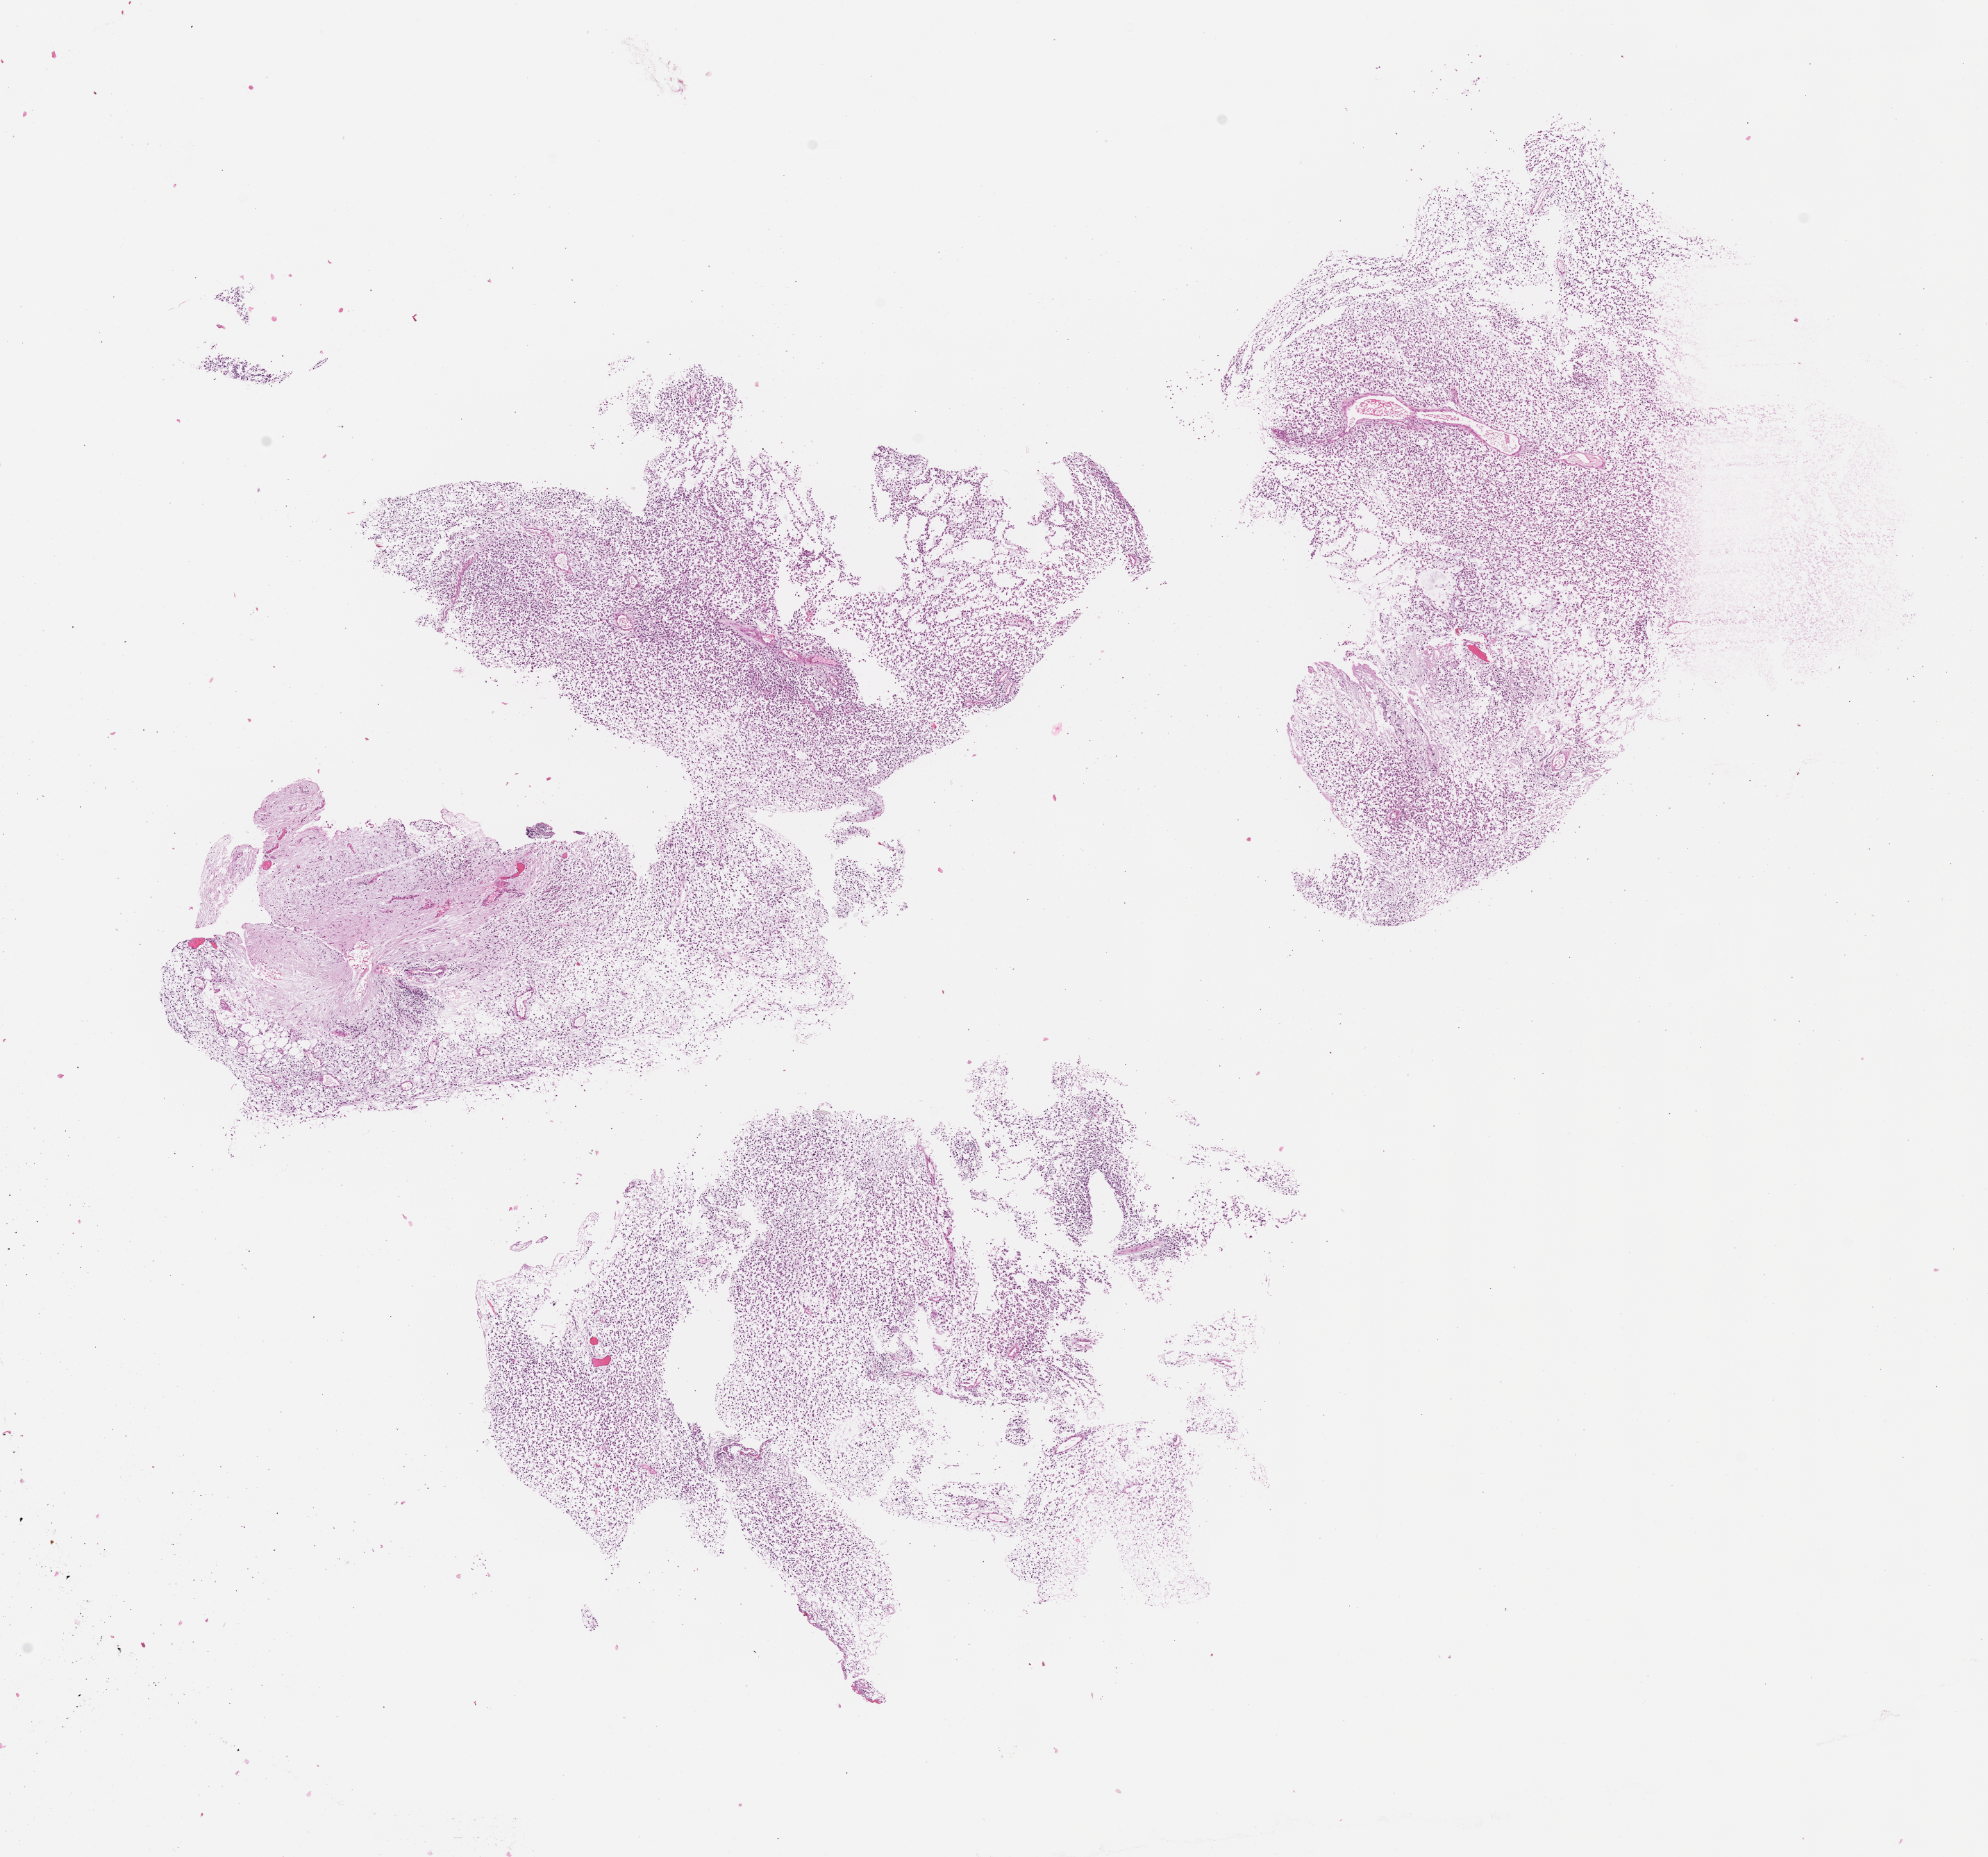
Hematoxylin and eosin (H&E) whole-slide image of tumor tissue, shown as a low-resolution overview of the whole scanned area (about 11.6 x 10.8 mm); FFPE section; site: eye, orbit-right. Patient: female, age 23.4 years at diagnosis.
Stage (as recorded): 1. Metastatic status at presentation (as recorded): non-metastatic. Diagnosis: rhabdomyosarcoma; histological classification: embryonal rhabdomyosarcoma.